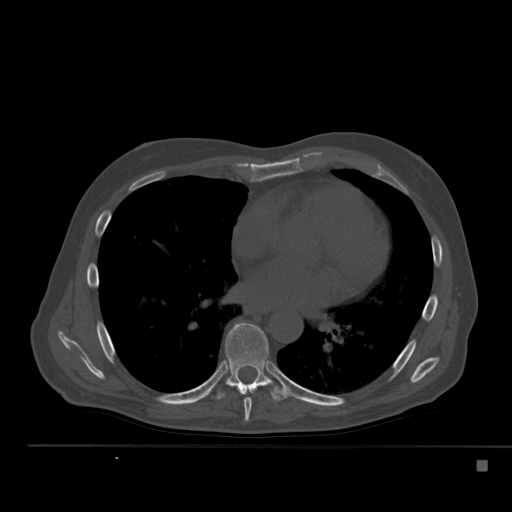
CT including the spine, one axial slice; slice 315 of 517 in the series (ordered by position); 120 kVp; bone window (W 1800 / L 400 HU); 1.5 mm slice thickness; 512 × 512 image matrix, field of view 408 × 408 mm. Patient: male, 70 years. Case-level facts recorded for this patient, not image findings: primary cancer: renal; vertebrae with lytic lesions (as recorded): T4, T6, T10, T12, L3, L4, L5.
Annotated regions visible in this slice (semi-automatically segmented with operator editing):
- T7 vertebra: box from (x=244, y=398) to (x=252, y=422) px
- T8 vertebra: (x=208, y=322)–(x=288, y=401)